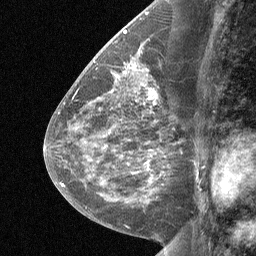
Breast MRI (dynamic contrast-enhanced), one sagittal slice. Position 31 of 64 along the scan axis. Dynamic contrast-enhanced study with each time point stored as its own series, time point 2 of 3 at this slice position (early post-contrast, ordered by acquisition time). 1.5 T. TE 4.8 ms, TR 27 ms. 2 mm slice thickness. 256 × 256 image matrix, field of view 180 × 180 mm. Patient: female, 59 years. Case-level facts recorded for this patient, not image findings: setting: breast cancer imaged before/during neoadjuvant chemotherapy; receptor status: triple-negative.
Structures marked on this image (semi-automatically segmented with operator editing):
- analysis volume of interest (the breast-tissue region the enhancement analysis was run in; not a lesion): bounding box [x1, y1, x2, y2] px = [127, 75, 173, 114]
- tumour enhancement mask (voxels above the 90 % enhancement threshold inside the analysis volume of interest): [148, 88, 157, 100]